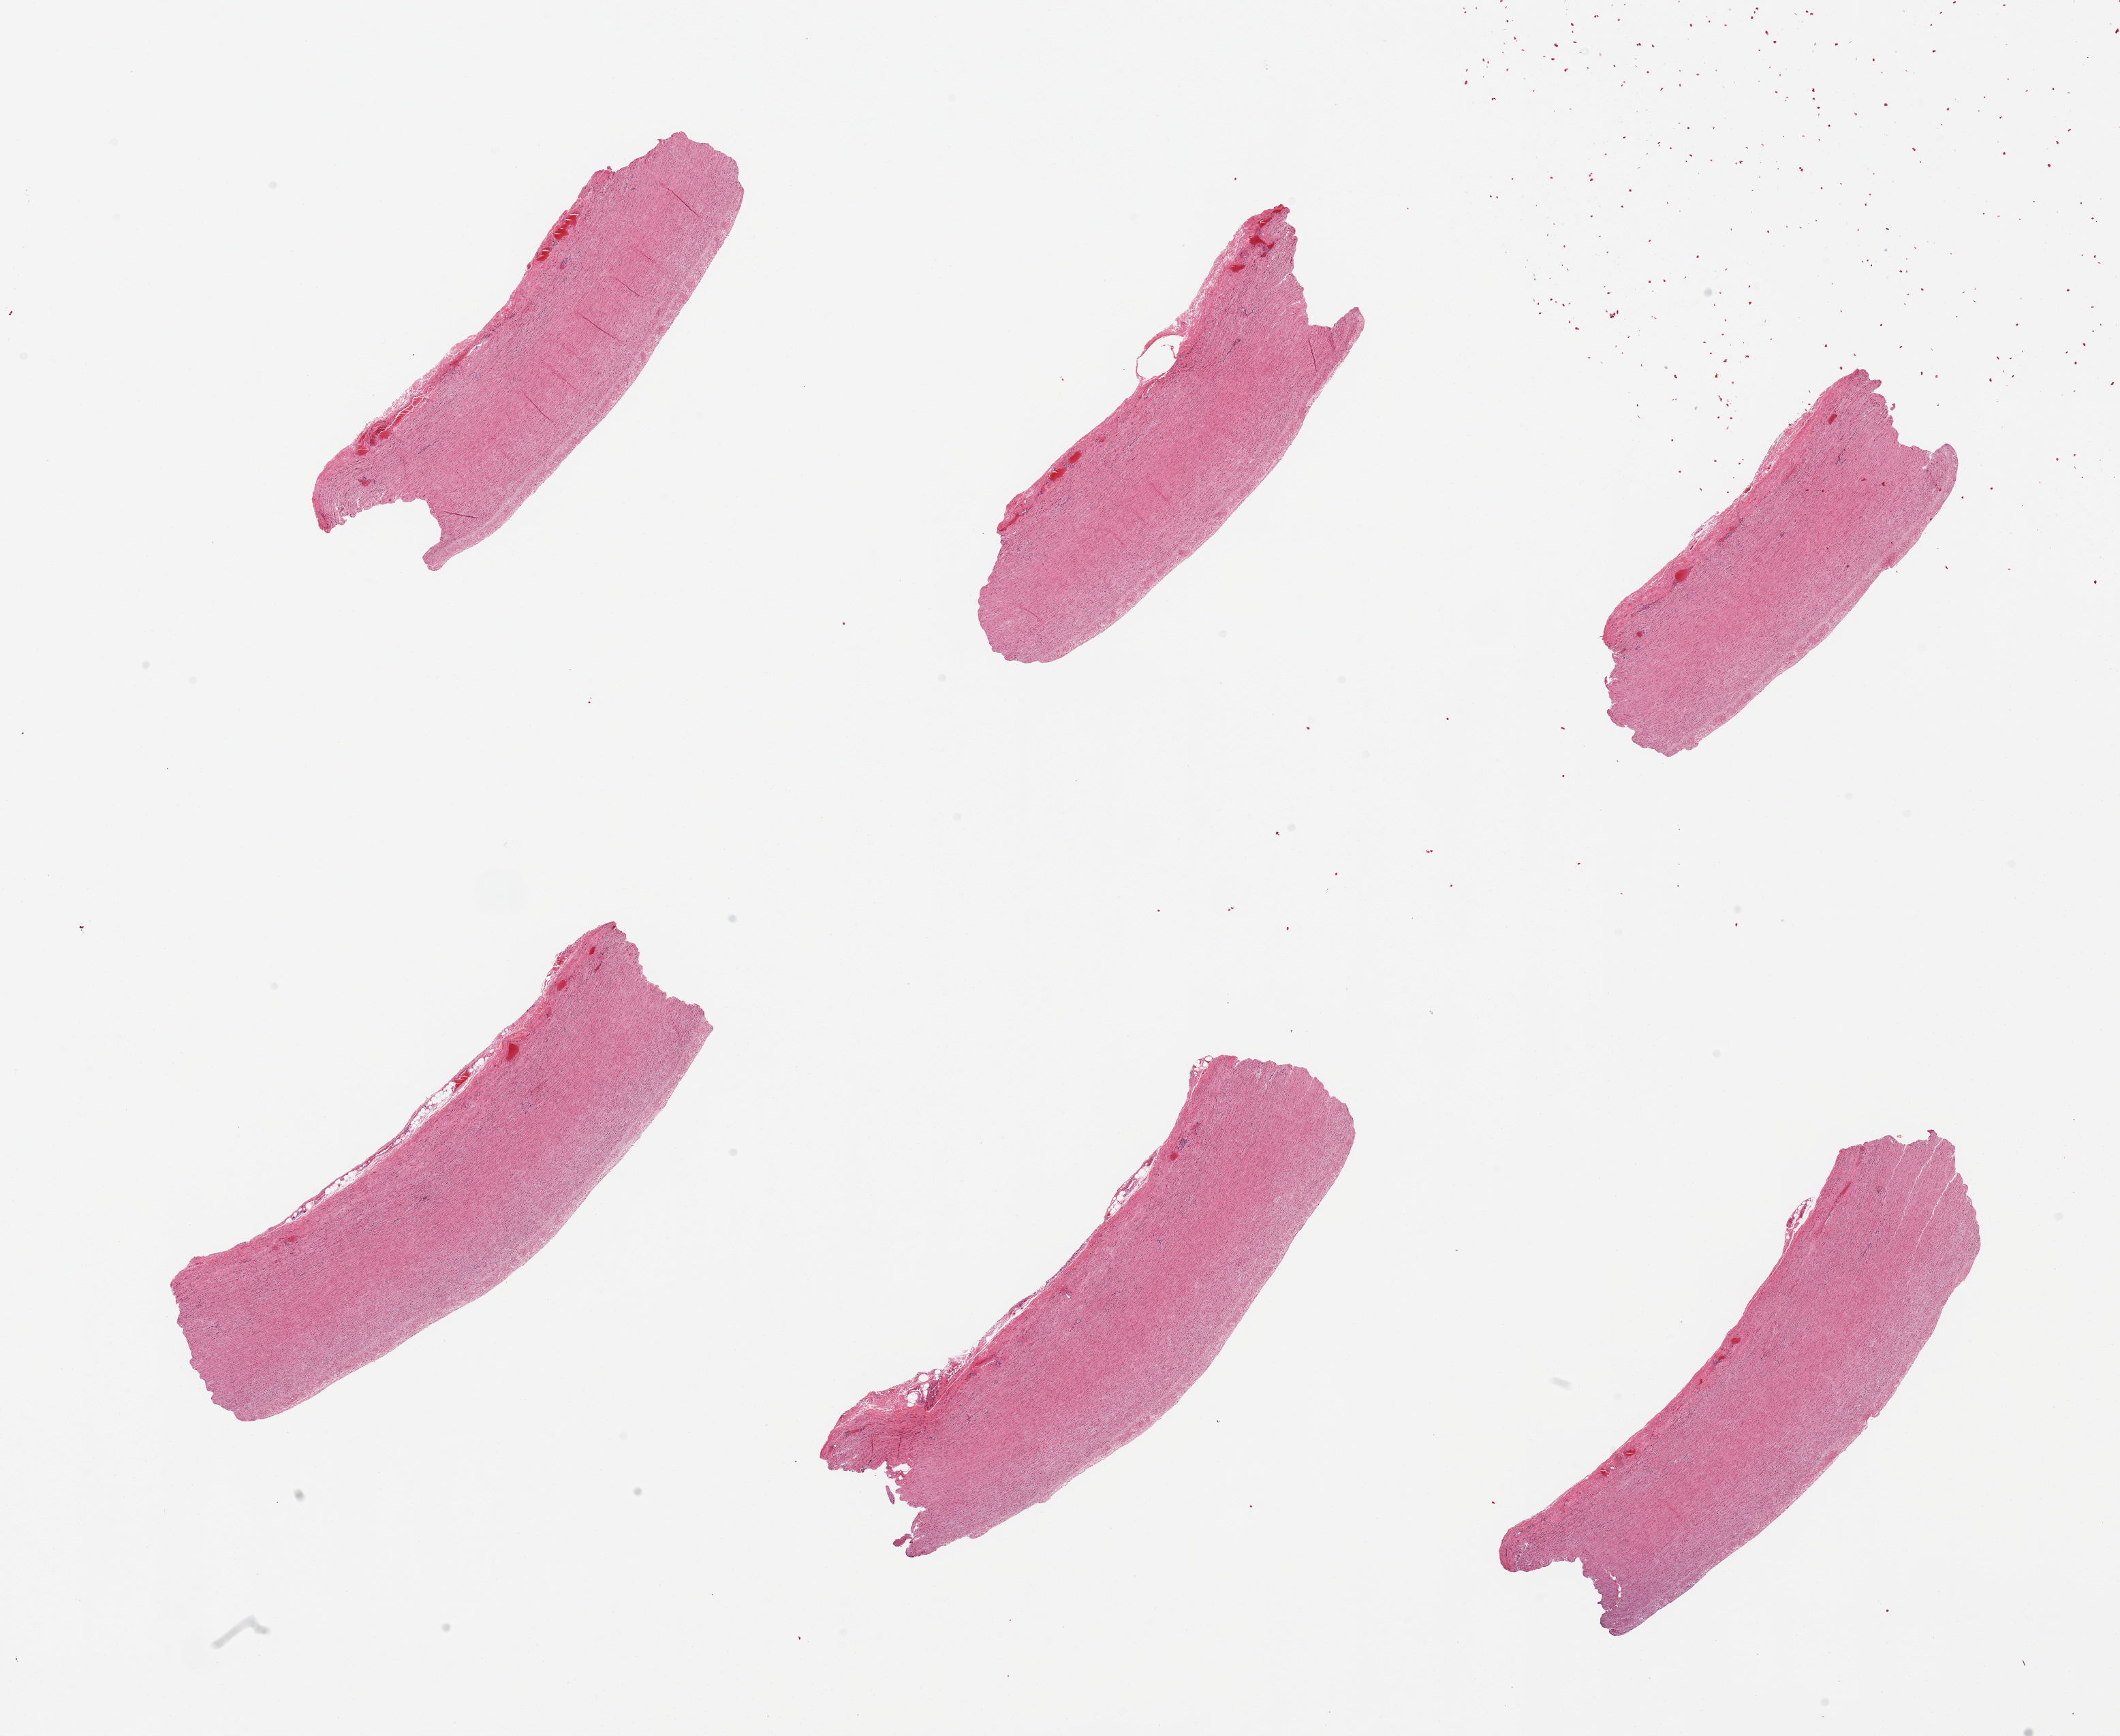
Digitized haematoxylin and eosin-stained section — whole scanned area (about 24.6 x 20.2 mm, acquisition: 20x scan) shown as a low-resolution overview. PAXgene-fixed, paraffin-embedded tissue. Target tissue: aorta. Tissue donor sample. Donor: male.
• review note (as recorded): 6 pieces; well trimmed